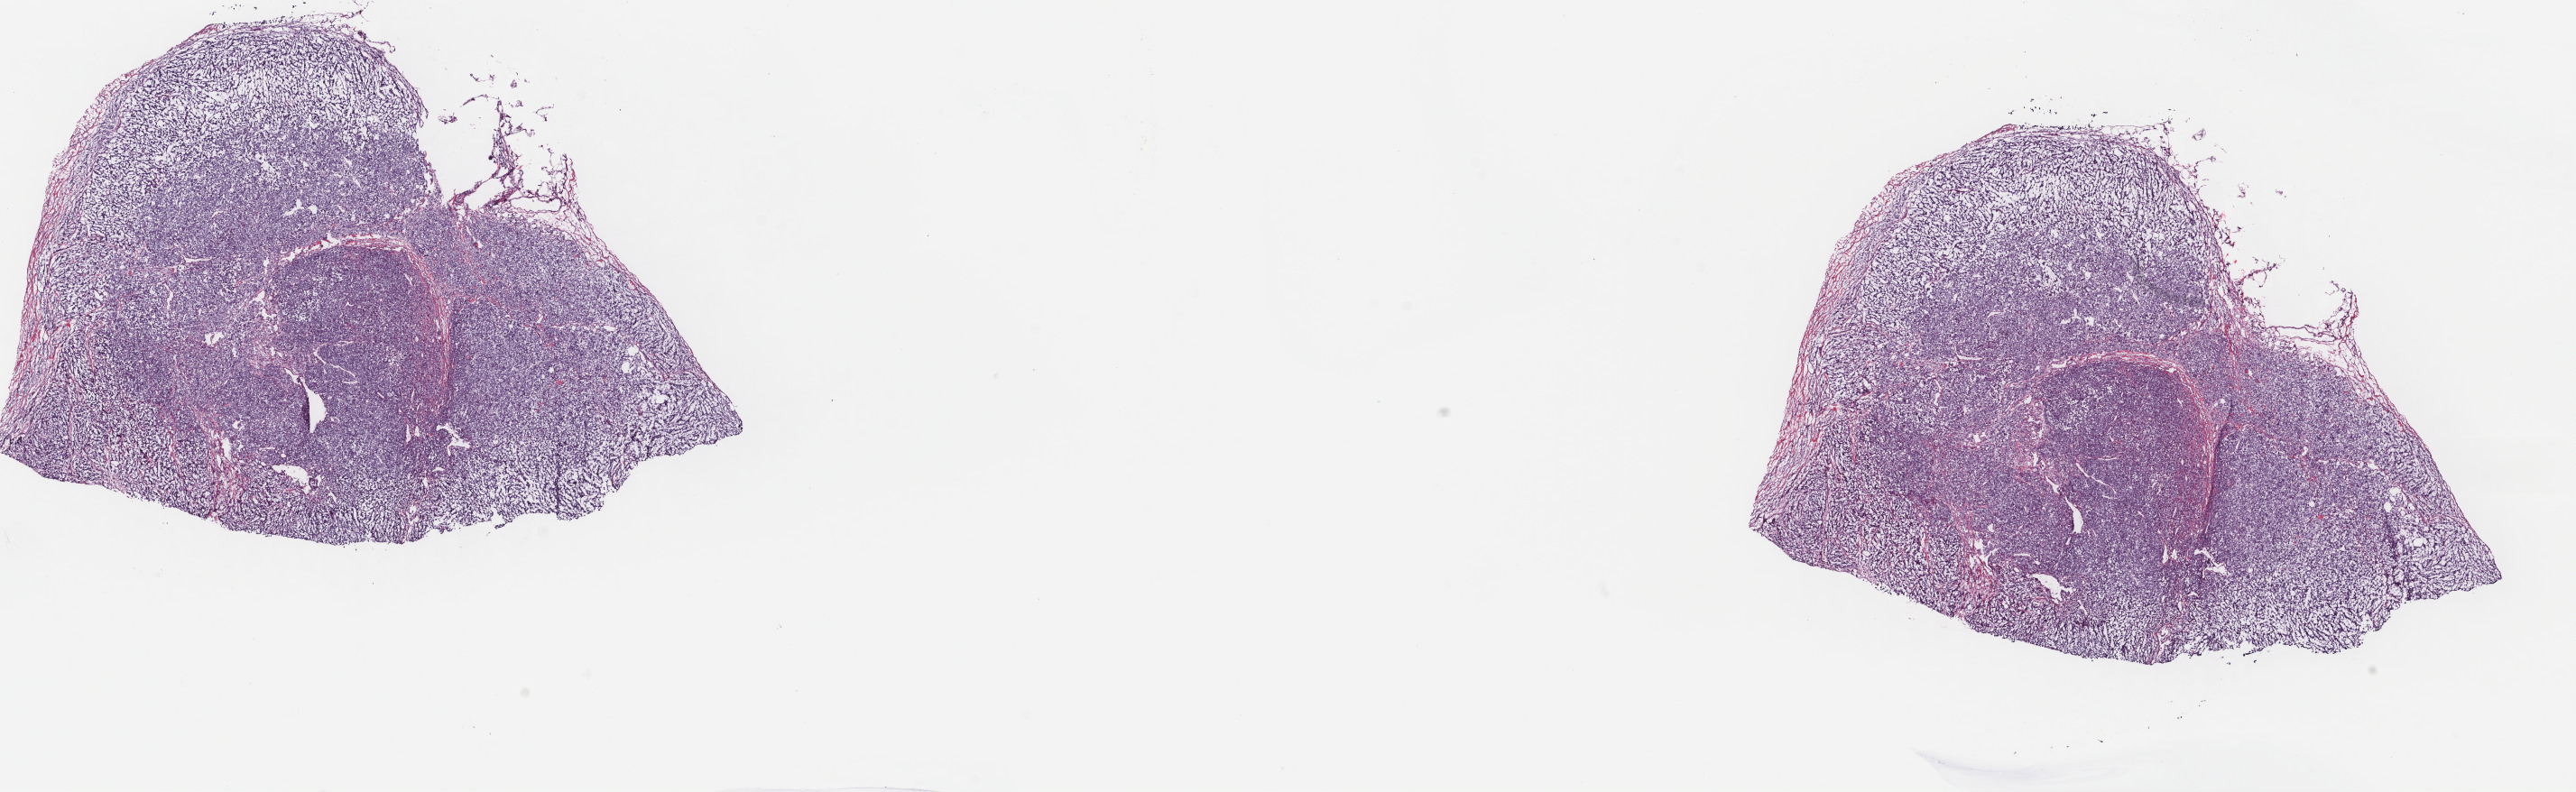
Digitized Hematoxylin and eosin (H&E) stained tissue section (whole slide) — whole scanned area (about 22.7 x 7.0 mm, from a 40x scan) shown as a low-resolution overview. Frozen section from the top of the tissue portion. Metastatic tumour sample. Male, age 43 years at initial diagnosis. Composition of this section per pathologist review: tumour cells 83%, tumour nuclei 90%, normal cells 0%, stromal cells 7%, necrosis 10%. Infiltration values recorded for this section: lymphocyte infiltration 5%, monocyte infiltration 1%, neutrophil infiltration 0%.
- this section: metastatic tumour tissue
- patient diagnosis: Malignant melanoma, NOS